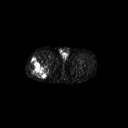
FDG PET of an extremity soft-tissue mass (from a PET/CT study), one axial slice. Slice 264 of 267 in the series (ordered by position). 3.27 mm slice thickness. 128 × 128 image matrix, field of view 700 × 700 mm. Patient: male, 43 years. From the clinical record (not read from this slice): histological type: poorly differentiated synovial sarcoma; grade: high; site of the primary tumour: right buttock.
Annotated regions visible in this slice (expert contour drawn on MRI and transferred to this co-registered scan by the dataset authors):
- gross tumour volume including surrounding oedema: bounding box (x1, y1, x2, y2) in pixels: (28, 58, 50, 78)
- gross tumour volume (mass): (29, 58, 48, 78)